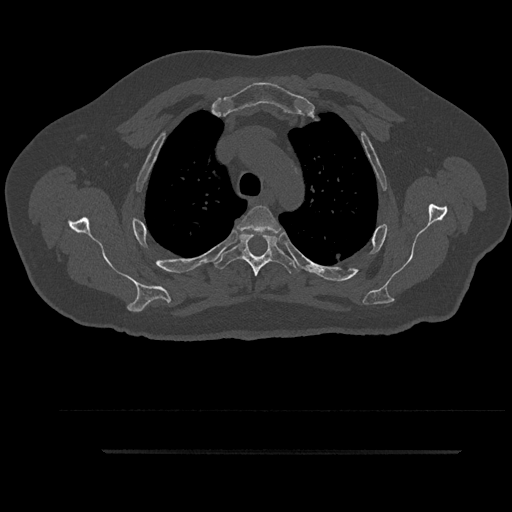
CT including the spine, one axial slice; position 688 of 797 along the scan axis; 120 kVp; bone window (W 1800 / L 400 HU); 0.5 mm slice thickness; 512 × 512 image matrix, field of view 432 × 432 mm. Male patient, age 63 years. Case-level facts recorded for this patient, not image findings: primary cancer: renal.
Annotated regions visible in this slice (semi-automatic segmentation, software-assisted and operator-edited):
- T3 vertebra: box from (x=237, y=206) to (x=281, y=236) px
- T4 vertebra: (x=213, y=234)–(x=300, y=276)